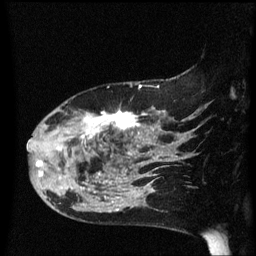
Breast MRI (dynamic contrast-enhanced), one sagittal slice. Slice 44 of 60 in the series (ordered by position). Dynamic contrast-enhanced series, image 2 of 3 at this slice position (ordered by acquisition). 1.5 T. TE 4.2 ms, TR 8.4 ms. 256 × 256 image matrix, field of view 200 × 200 mm. Patient: female, 47 years.
Outlined on this slice (semi-automatic segmentation, software-assisted and operator-edited):
- analysis volume of interest (the breast-tissue region the enhancement analysis was run in; not a lesion): bounding box [x1, y1, x2, y2] px = [28, 97, 149, 206]
- tumour enhancement mask (voxels above the 70 % enhancement threshold inside the analysis volume of interest): [28, 111, 147, 206]